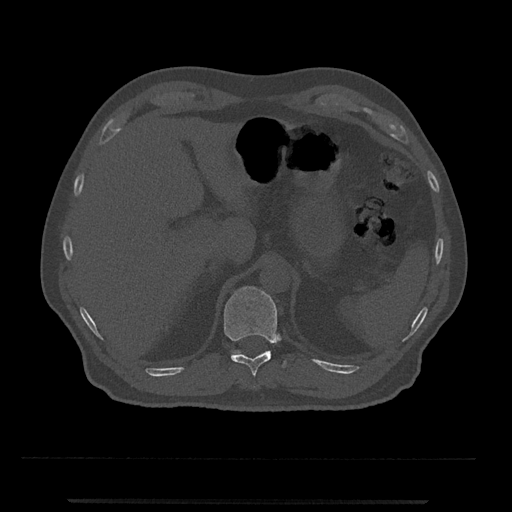
CT including the spine, one axial slice; slice 456 of 797 in the series (ordered by position); reconstruction kernel Br40s/3; bone window (W 1800 / L 400 HU); 0.5 mm slice thickness; 512 × 512 image matrix. Patient: male, 63 years. From the clinical record (not read from this slice): primary cancer: prostate.
Annotated regions visible in this slice (semi-automatic segmentation, software-assisted and operator-edited):
- T11 vertebra: box from (x=223, y=286) to (x=286, y=387) px
- T12 vertebra: (x=232, y=350)–(x=241, y=355)